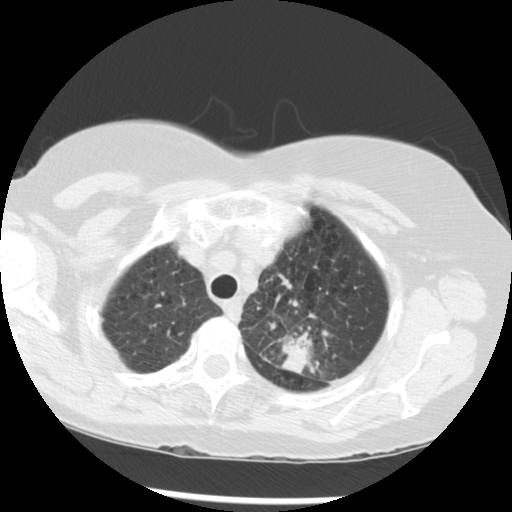
Low-dose screening chest CT, one axial slice. Position 238 of 283 along the scan axis. Lung window (W 1500 / L -600 HU). 2.5 mm slice thickness. 512 × 512 image matrix, field of view 330 × 330 mm.
Annotated regions visible in this slice (expert manual segmentation):
- lesion 1 (tumor, upper lobe of left lung): bounding box (x1, y1, x2, y2) in pixels: (280, 330, 315, 374)